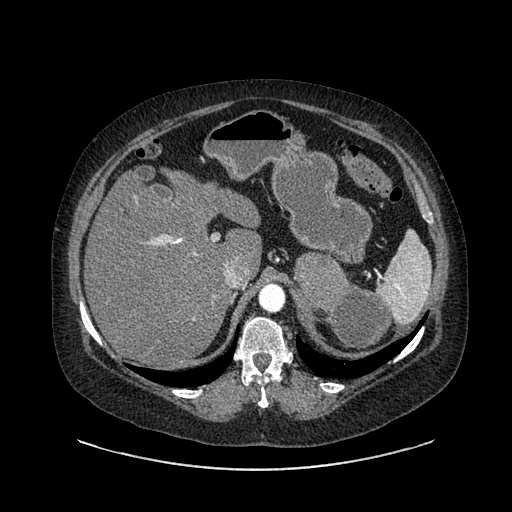
Contrast-enhanced abdominal CT, one axial slice. Slice 614 of 769 in the series (ordered by position). Reconstruction kernel SOFT. Soft-tissue window (W 400 / L 40 HU). 0.62 mm slice thickness. 512 × 512 image matrix, field of view 460 × 460 mm. Female patient, age 61 years. From the clinical record (not read from this slice): diagnosis: adrenocortical carcinoma; tumour side: left adrenal; tumour size at pathology: 13 cm; Ki-67 index: 79 %; stage (as recorded): 2.
Annotated regions visible in this slice (semi-automatic segmentation, software-assisted and operator-edited):
- mass: bounding box [x1, y1, x2, y2] px = [295, 254, 392, 350]